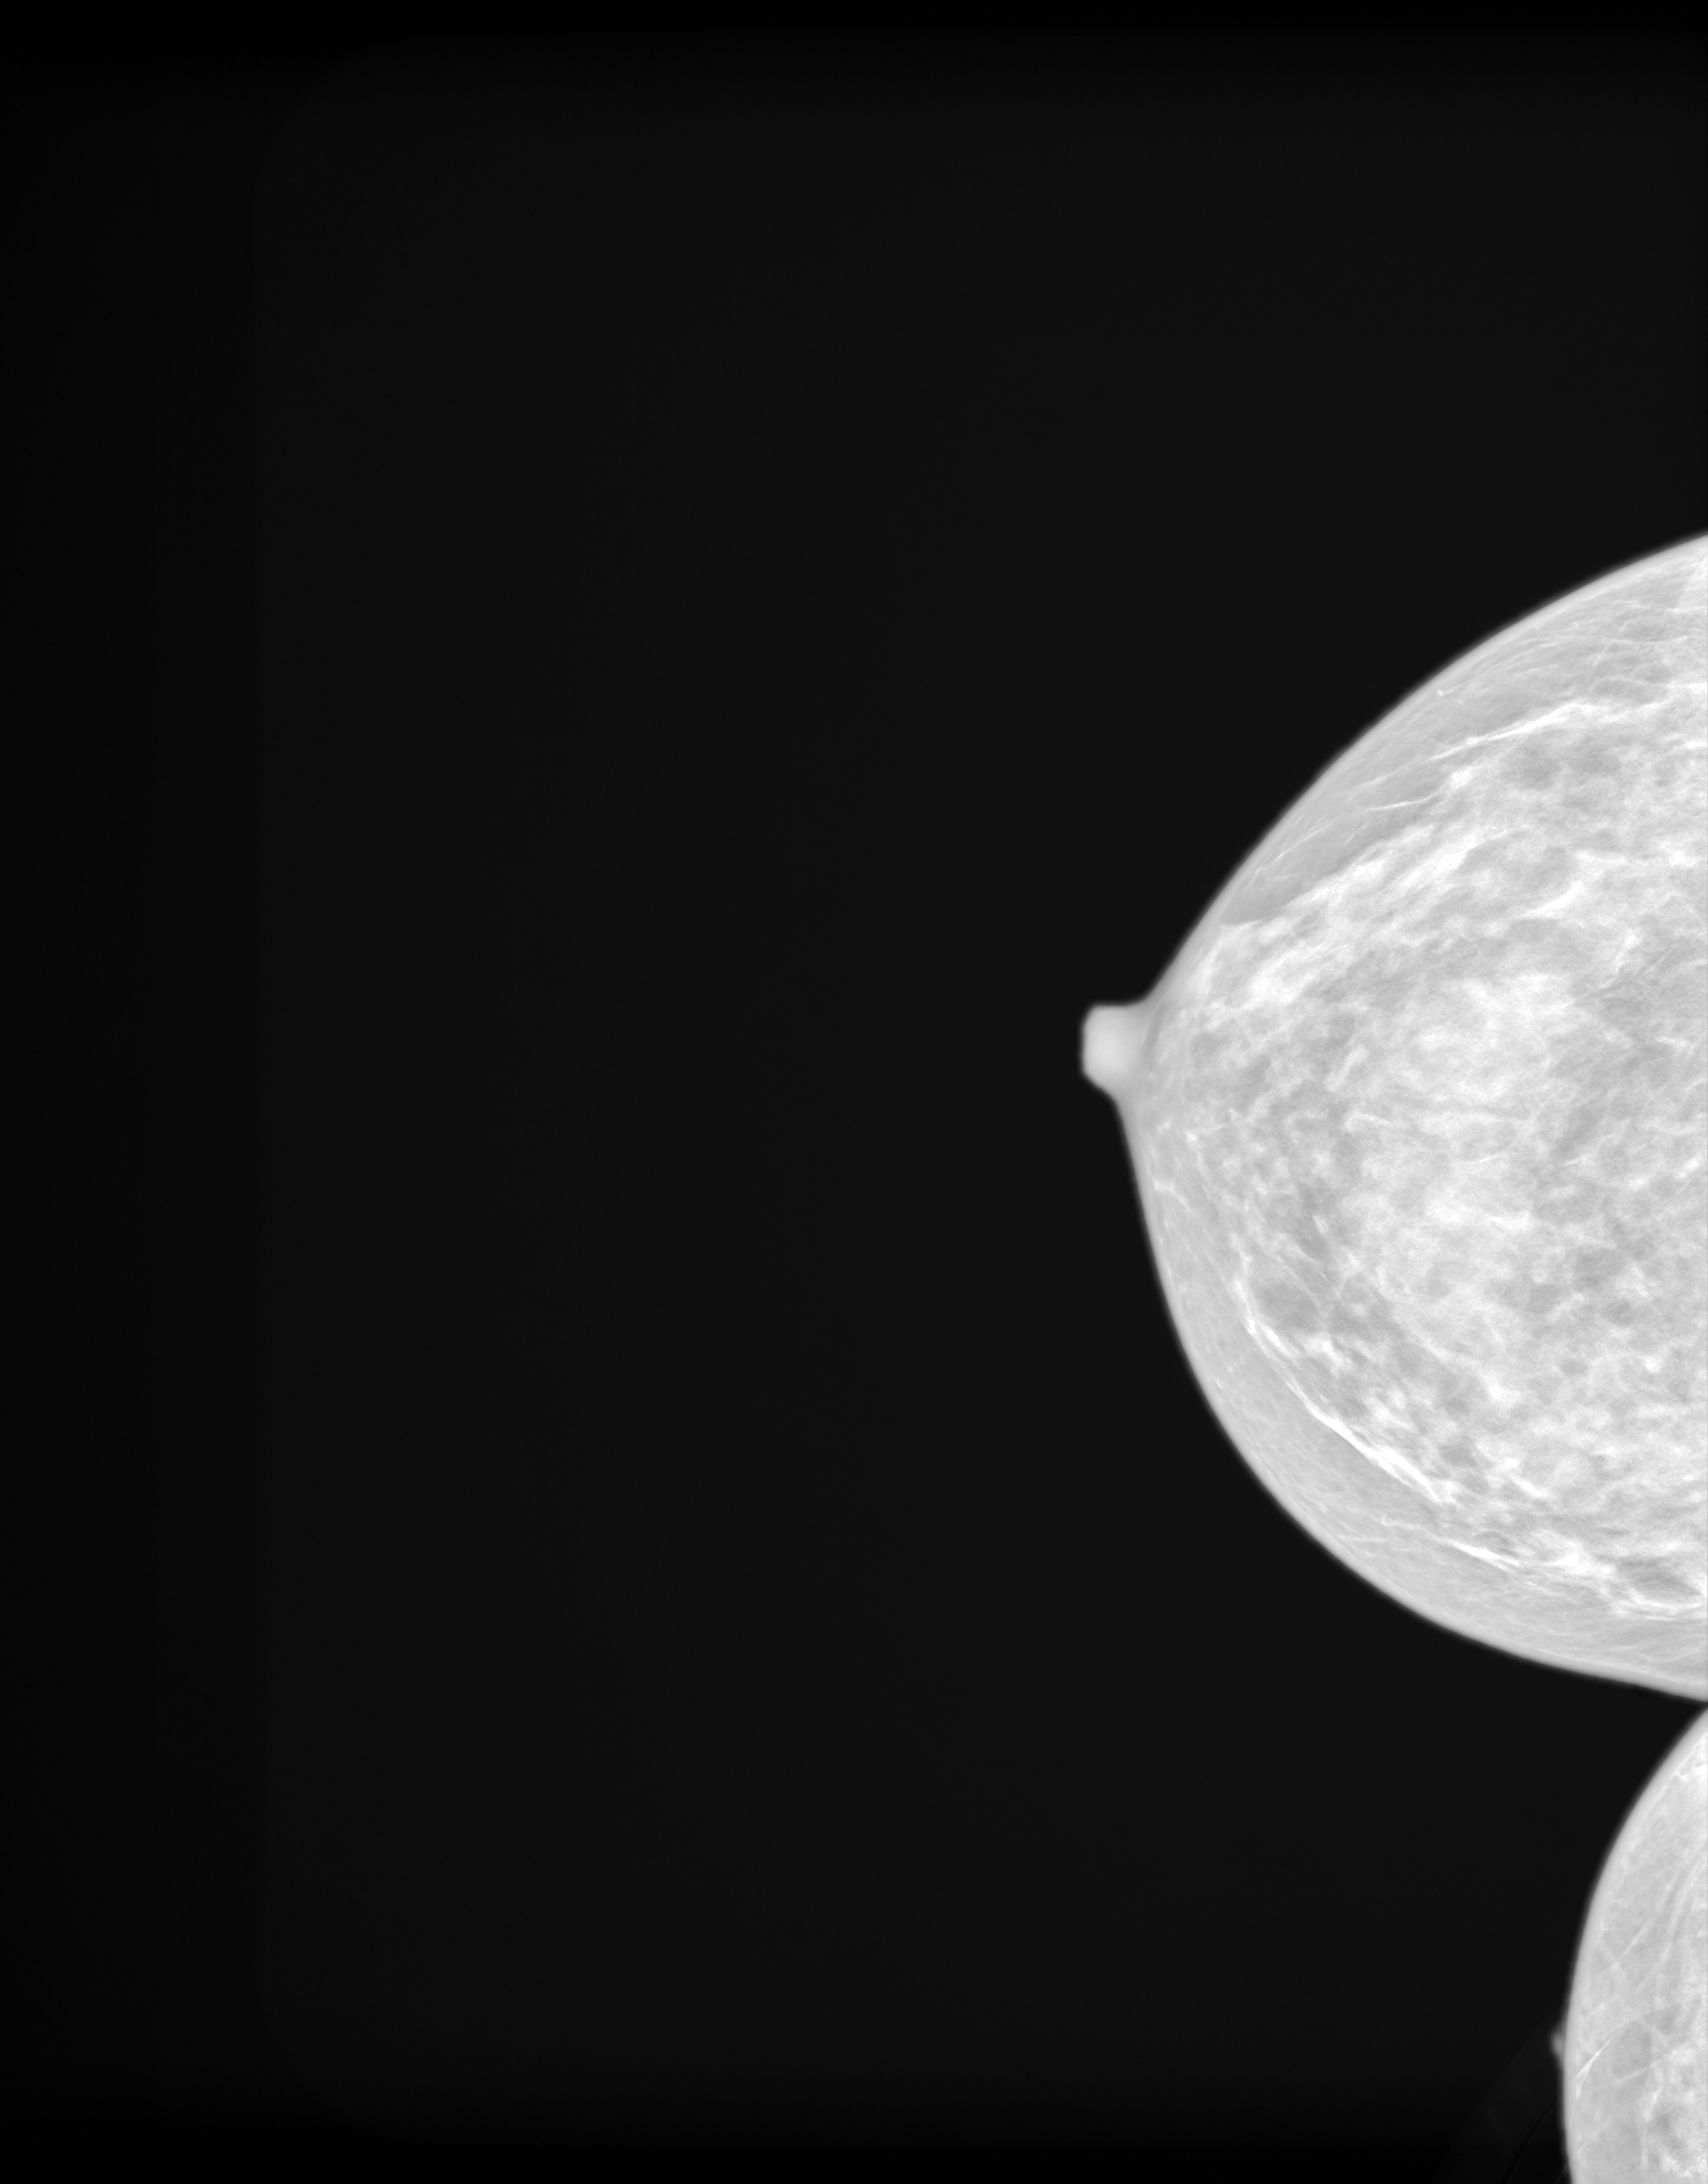
Annual screening mammography examination; system: SenoIris_1SP2(440). Patient aged 61 years (female).
Image type: synthesized 2-D view from tomosynthesis. Breast: right. Projection: cranio-caudal projection.